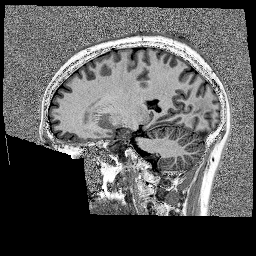
Brain MRI from a brain-tumour surgery series, one sagittal slice; slice 72 of 176 in the series (ordered by position); 1 mm slice thickness; 256 × 256 image matrix. Case-level facts recorded for this patient, not image findings: histopathology: Glioblastoma; WHO grade: 4; IDH mutation: no; tumour location: Left Frontal.
Structures marked on this image (expert manual segmentation):
- tumour: bounding box <133,68,147,83> (left, top, right, bottom; pixels)